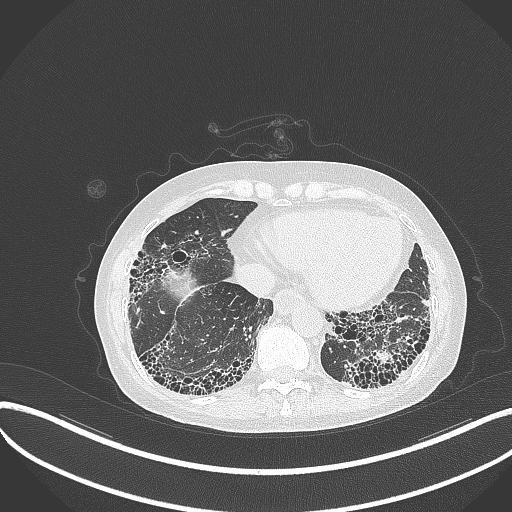
Chest CT, one axial slice; slice 77 of 373 in the series (ordered by position); lung window (W 1500 / L -600 HU); 1 mm slice thickness; 512 × 512 image matrix. Female patient, age 56 years. Case-level facts recorded for this patient, not image findings: clinical TNM (as recorded): T1 N0 M0.
Annotated regions visible in this slice (bounding box drawn by a radiologist):
- lung tumour (recorded histology: adenocarcinoma): box from (x=371, y=346) to (x=398, y=367) px